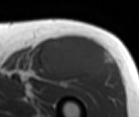
MRI of an extremity soft-tissue mass, one axial slice; MR volume resampled by the dataset authors to the PET/CT grid (not the native acquisition matrix); 3.27 mm slice thickness; 139 × 117 image matrix, field of view 136 × 114 mm. Male patient. From the clinical record (not read from this slice): histological type: extraskeletal osteosarcoma; grade: high; site of the primary tumour: thigh.
Structures marked on this image (expert contour drawn on MRI and transferred to this co-registered scan by the dataset authors):
- gross tumour volume (mass): bounding box (x1, y1, x2, y2) in pixels: (40, 37, 110, 79)